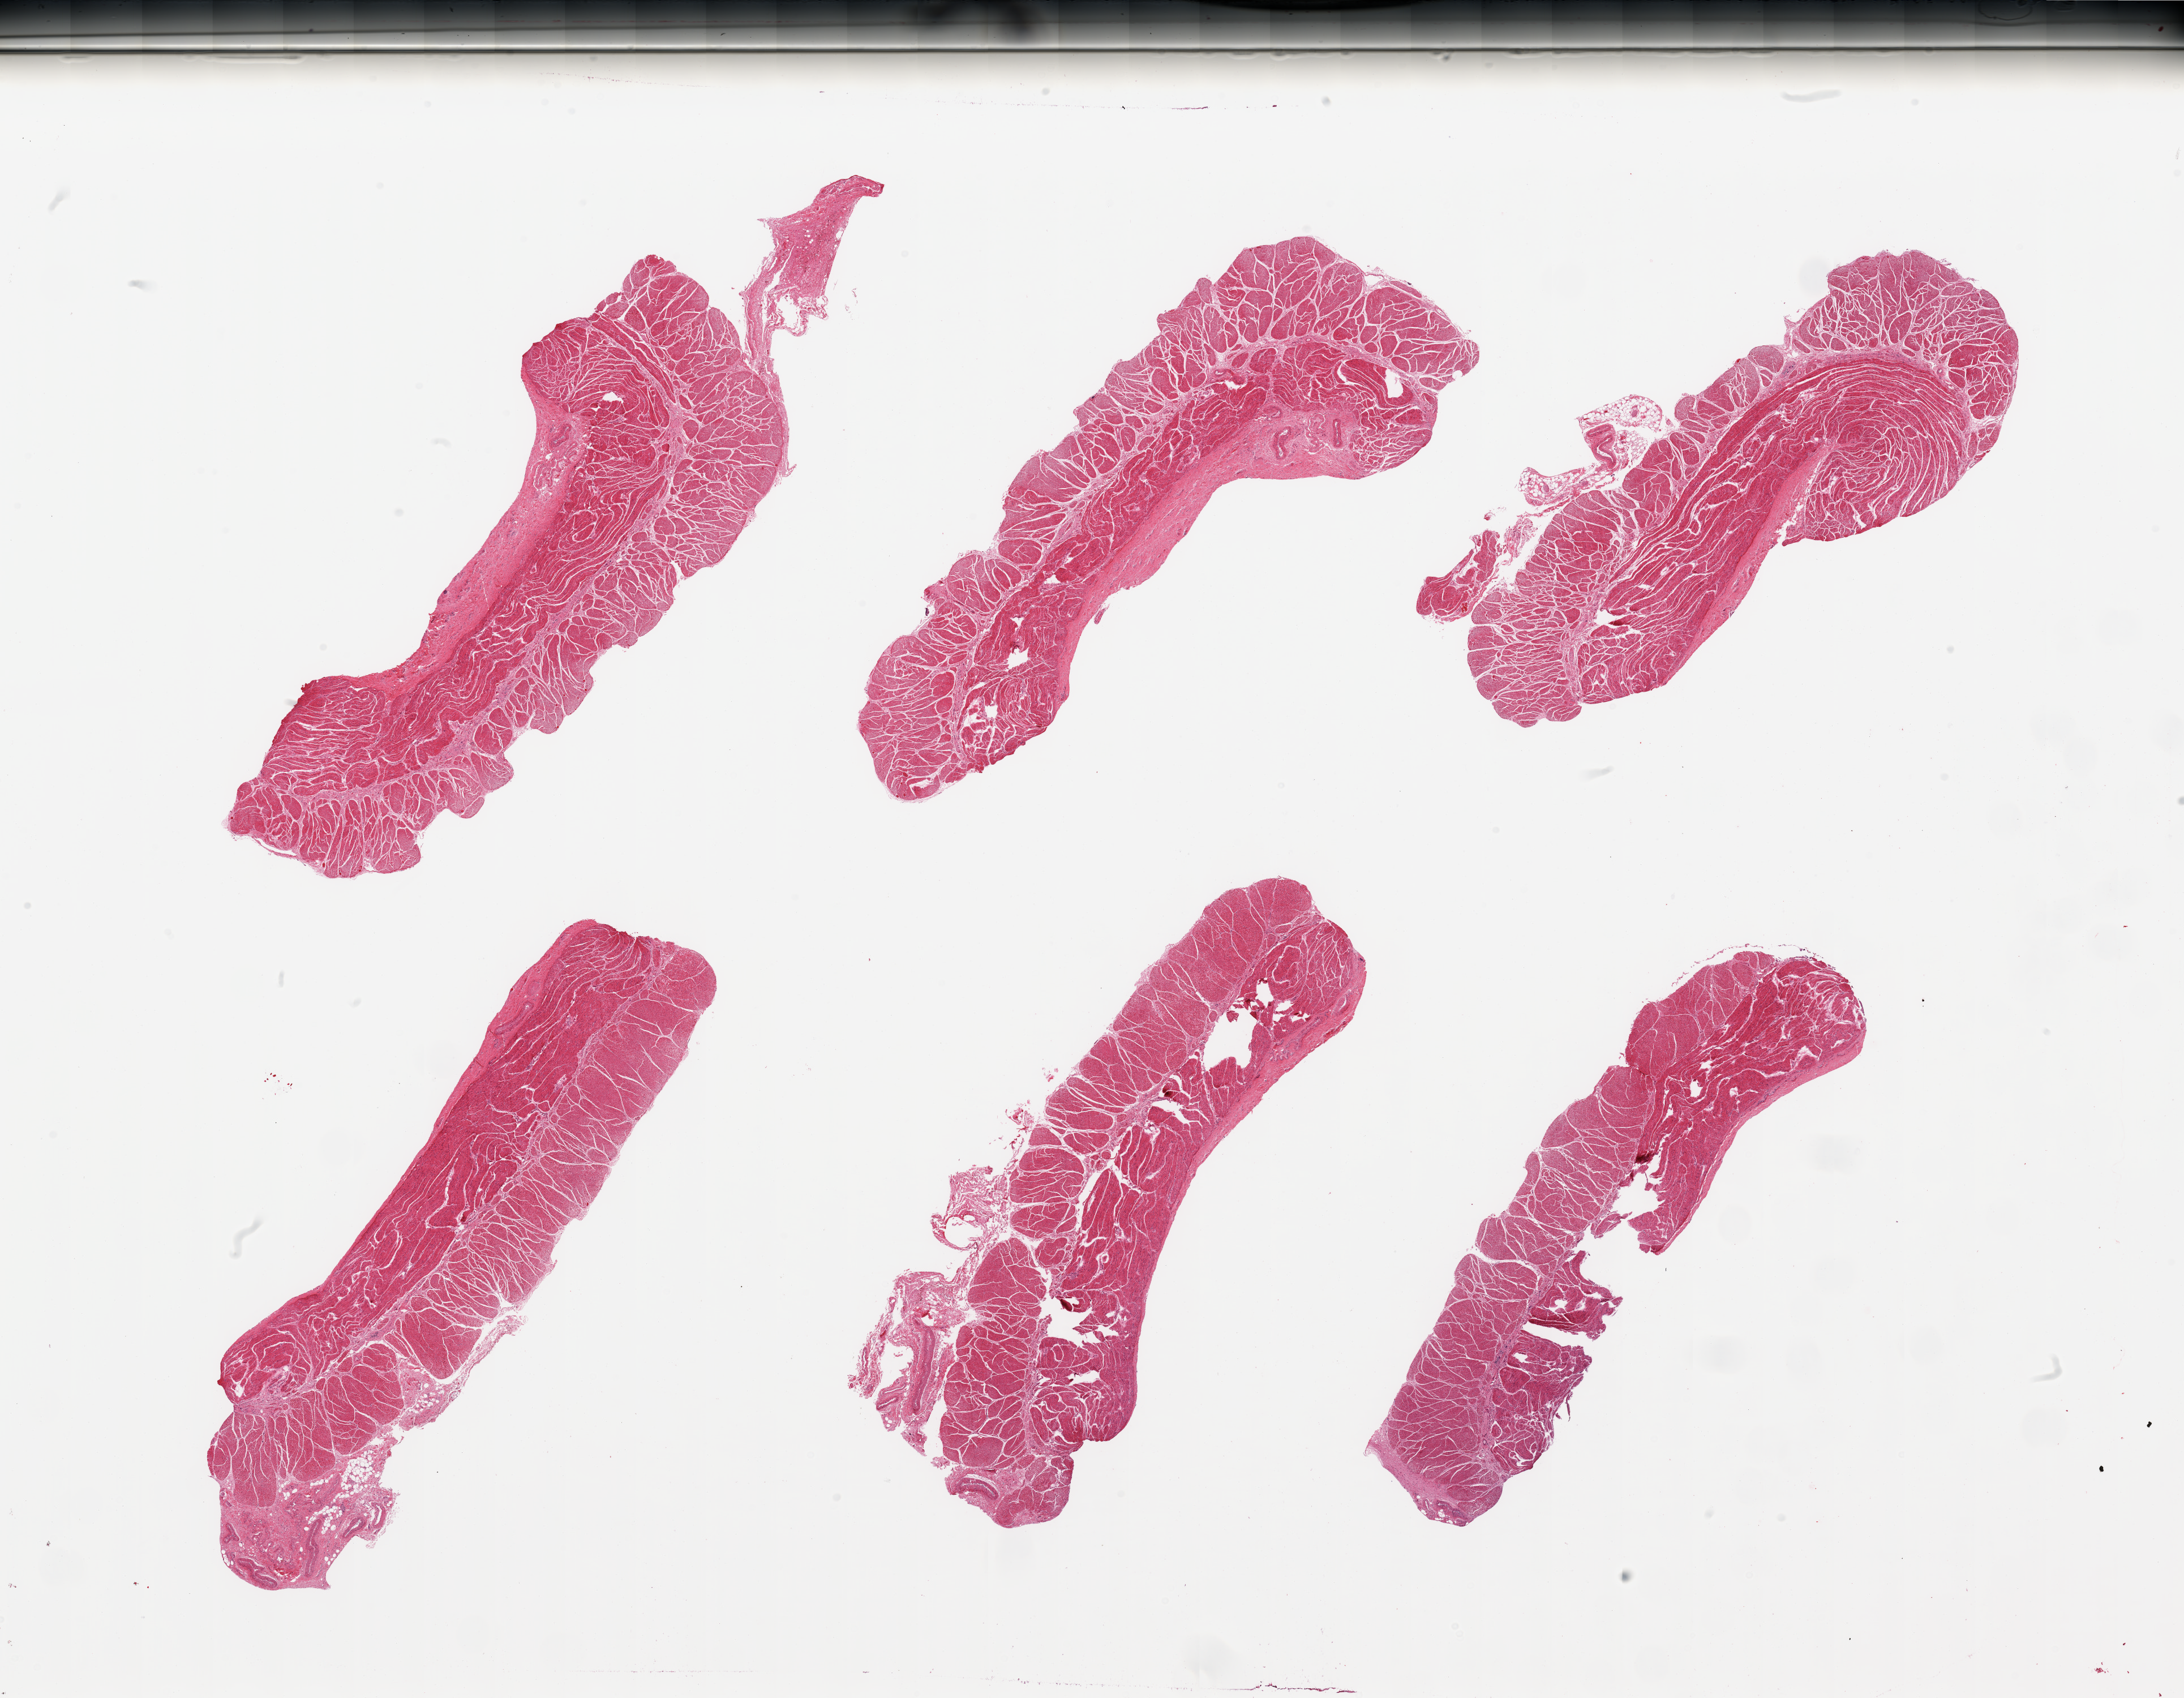
Hematoxylin and eosin (H&E) whole-slide image, brightfield, a low-resolution overview of the entire scanned area, about 30.5 x 23.7 mm, PAXgene-fixed paraffin-embedded (PFPE) section, section of esophageal muscle (target tissue), donor tissue sample. Donor: male.
Reviewer comment on this tissue sample: 6 pieces; well dissected.